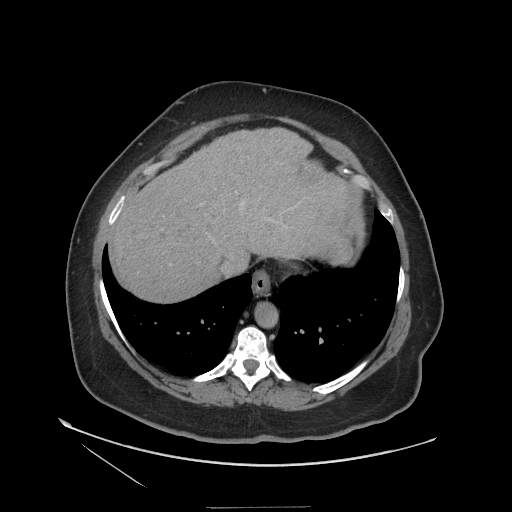
Contrast-enhanced abdominal CT (liver protocol), one axial slice. Slice 97 of 127 in the series (ordered by position). Reconstruction kernel STANDARD. 140 kVp. Soft-tissue window (W 400 / L 40 HU). 2.5 mm slice thickness. 512 × 512 image matrix. From the clinical record (not read from this slice): diagnosis: hepatocellular carcinoma (patient treated with transarterial chemoembolisation; whether this scan precedes or follows treatment is not stated here); TNM stage (as recorded): Stage-II; Child-Pugh class: A; tumour differentiation: well differentiated; tumour size: 3 cm.
Annotated regions visible in this slice (semi-automatically segmented with operator editing):
- abdominal aorta: bounding box (x1, y1, x2, y2) in pixels: (255, 302, 277, 326)
- liver parenchyma outside the tumour (the mass and vessels are separate outlines, so this box may not span the whole liver): (110, 128, 364, 300)
- liver vessels: (118, 203, 244, 212)